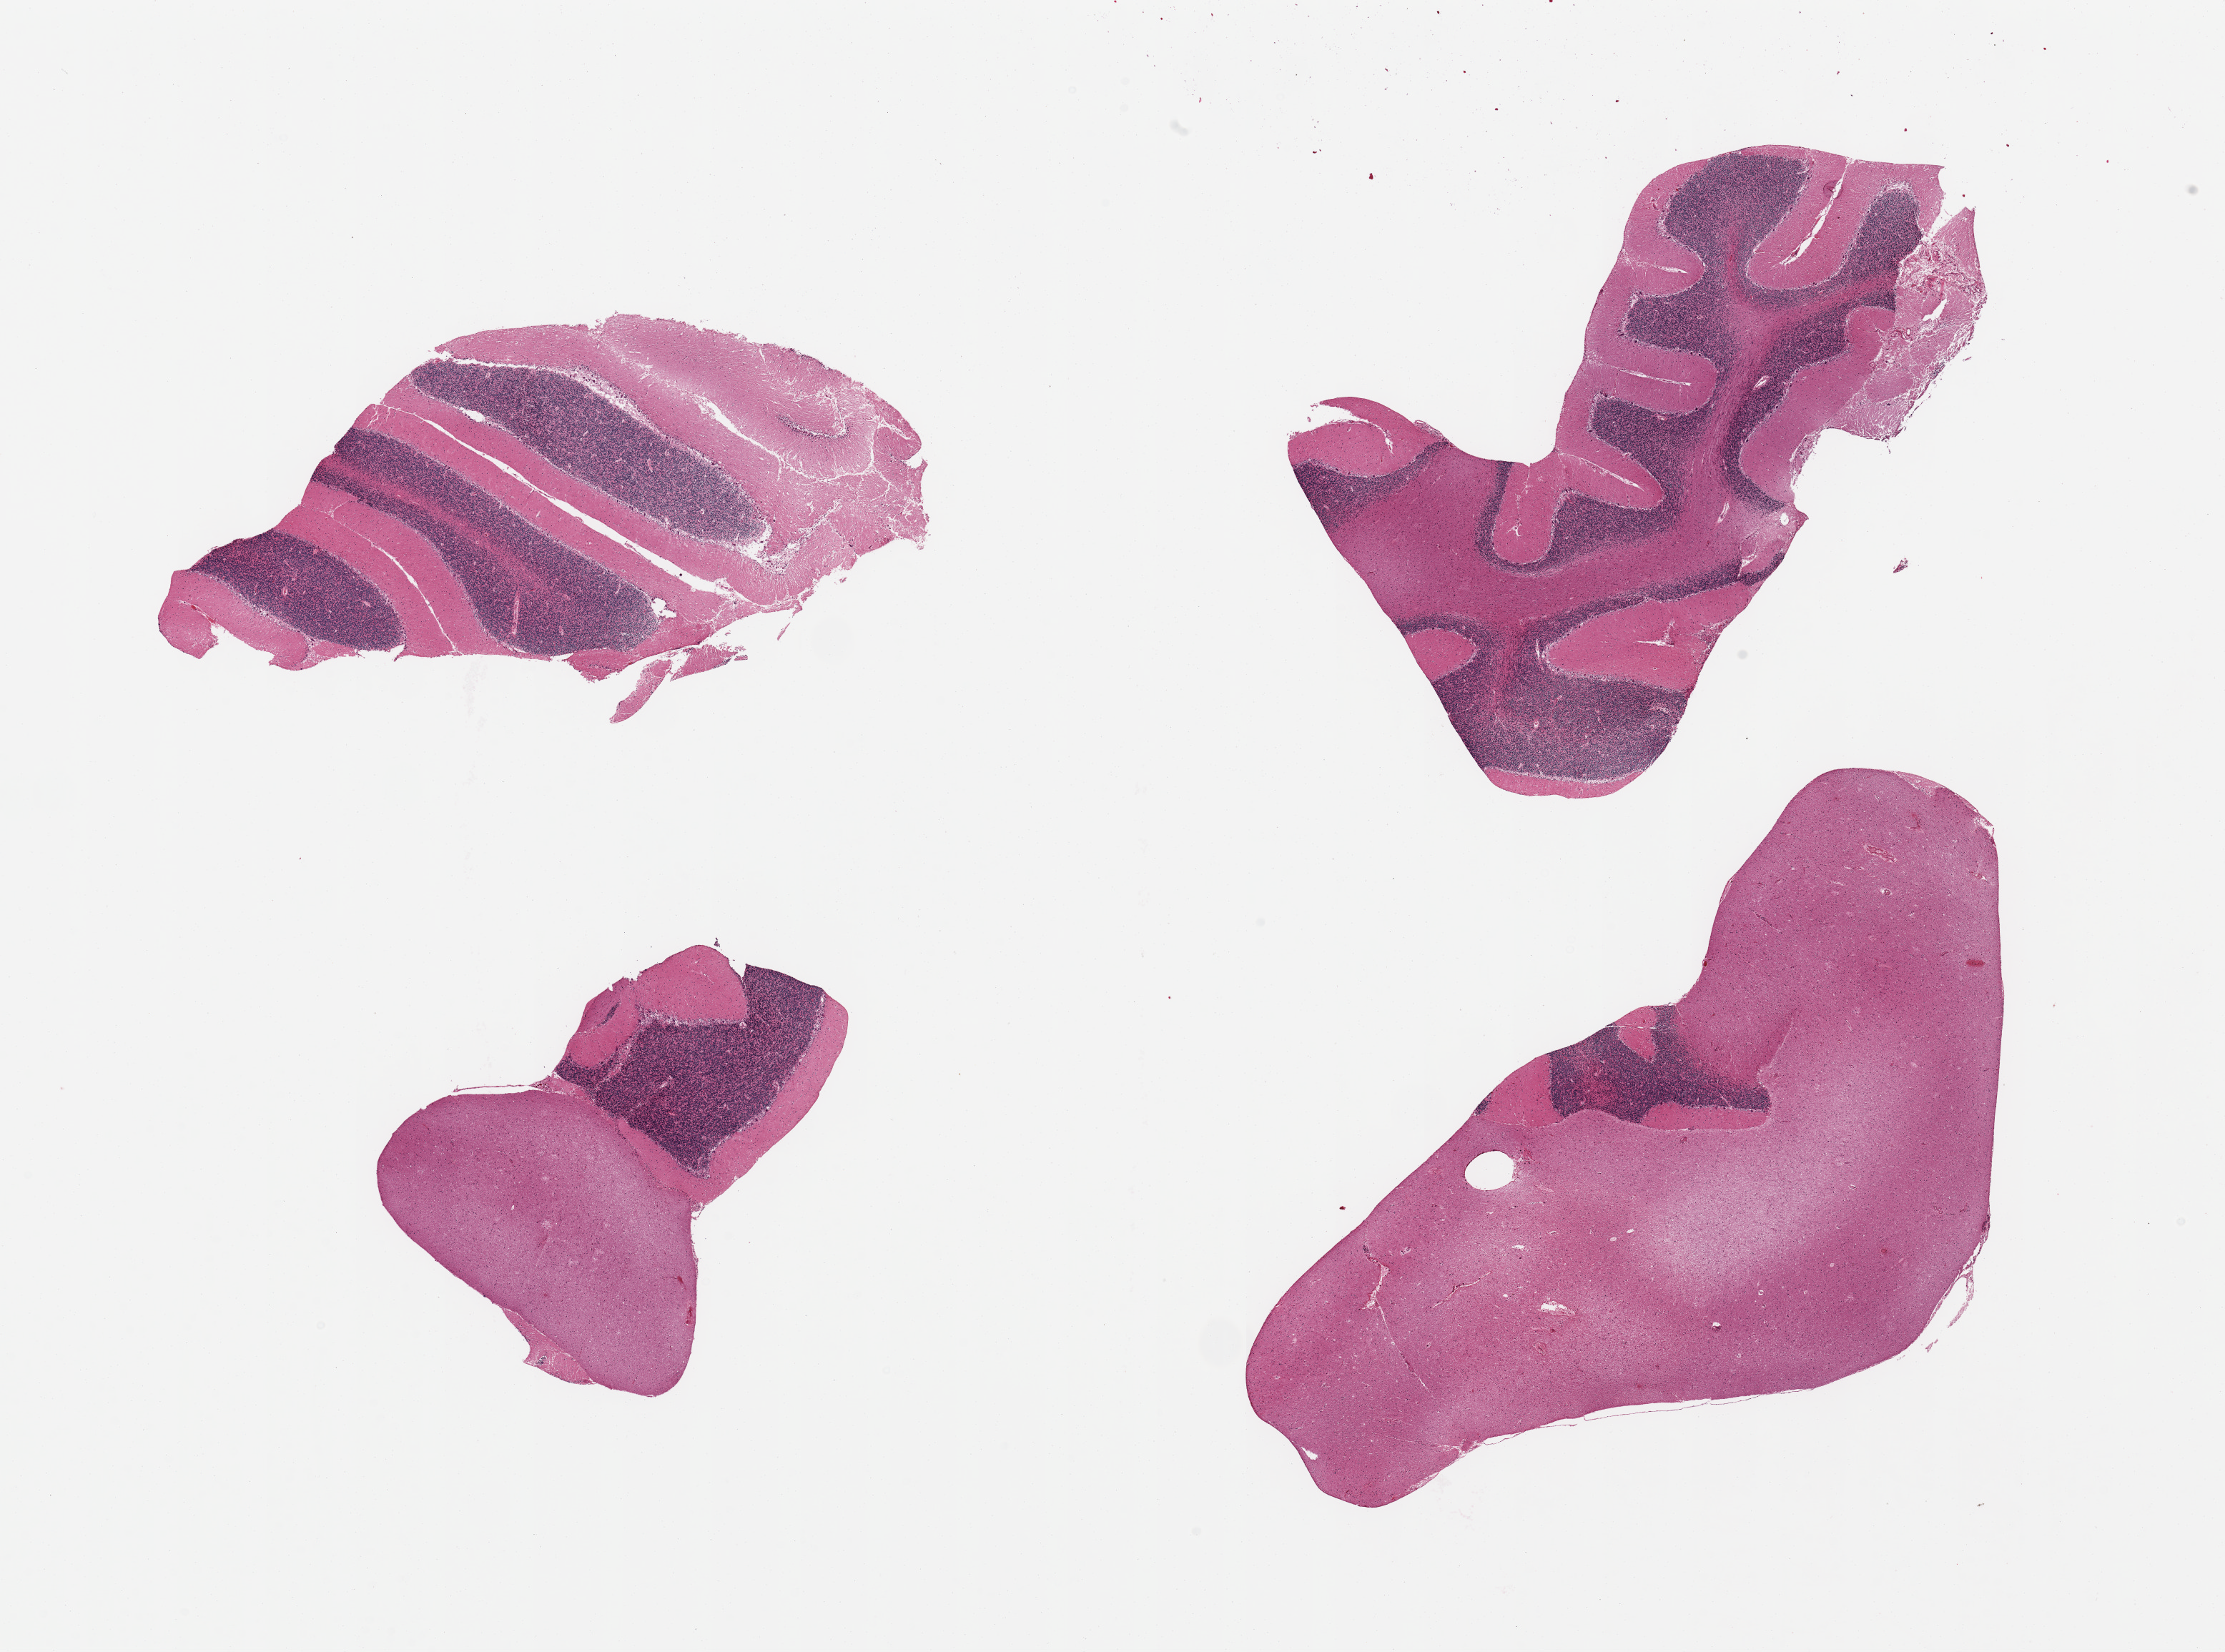
H&E whole-slide image, brightfield, shown as a low-resolution overview of the whole scanned area (about 24.6 x 18.3 mm). PAXgene-fixed paraffin-embedded (PFPE) section. Section of cerebellum (target tissue). Donor tissue sample.
• review note (as recorded): 4 pieces; 2 are largely white matter